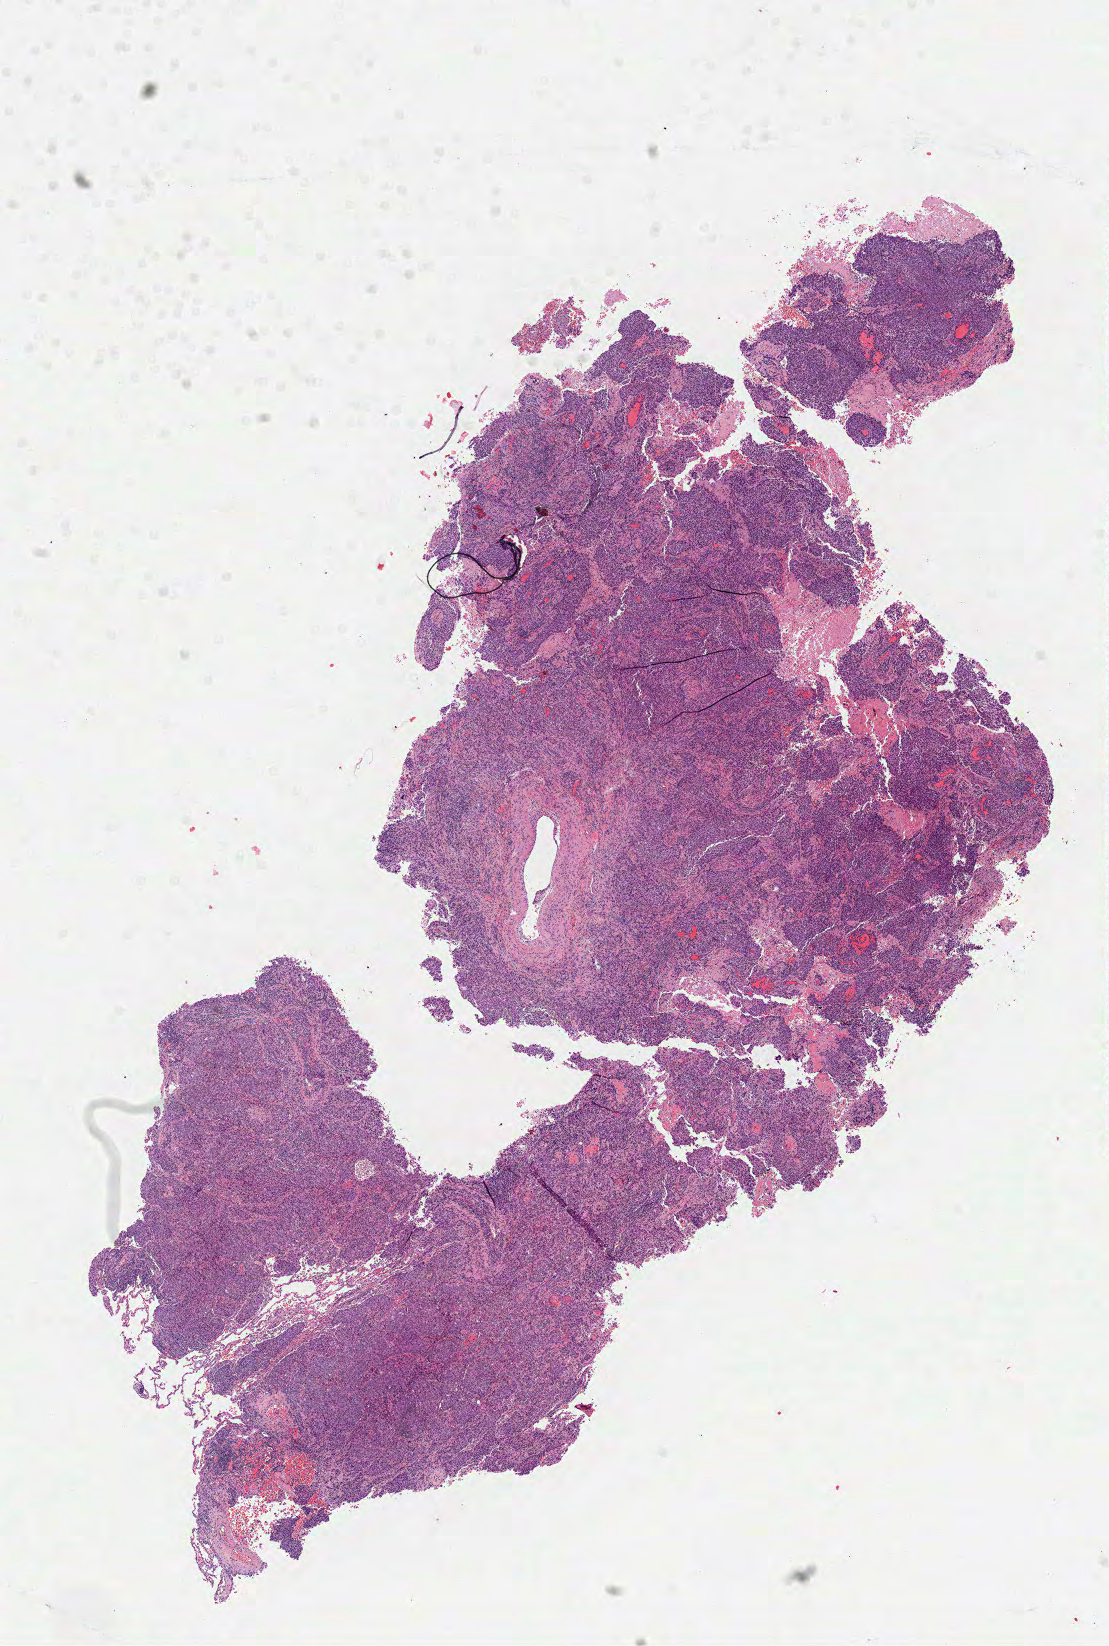
Whole-slide histology image, H&E, whole scanned area (about 8.9 x 13.3 mm, slide scanned at 40x) shown as a low-resolution overview. Frozen section. Sample: primary tumour, lung. Male, age 56 years at initial diagnosis. Composition of this section per pathologist review: tumour cells 95%, tumour nuclei 61%, normal cells 0%, stromal cells 0%, necrosis 5%. Infiltration values recorded for this section: lymphocyte infiltration 30%, monocyte infiltration 0%, neutrophil infiltration 0%.
AJCC pathologic stage: IIB. Diagnosis: Squamous cell carcinoma, NOS (upper lobe, lung). TNM: T2b N1 MX.